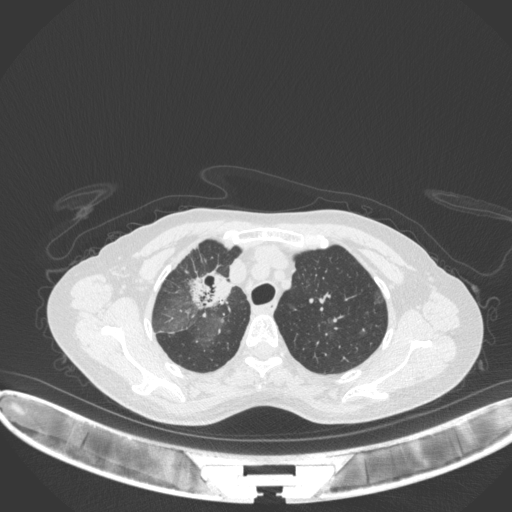
Chest CT, one axial slice; position 254 of 311 along the scan axis; reconstruction kernel B31f; lung window (W 1500 / L -600 HU); 512 × 512 image matrix, field of view 400 × 400 mm. Patient: female, 59 years. From the clinical record (not read from this slice): clinical TNM (as recorded): T3 N0 M0.
Outlined on this slice (bounding box drawn by a radiologist):
- lung tumour (recorded histology: adenocarcinoma): bounding box <184,256,236,319> (left, top, right, bottom; pixels)